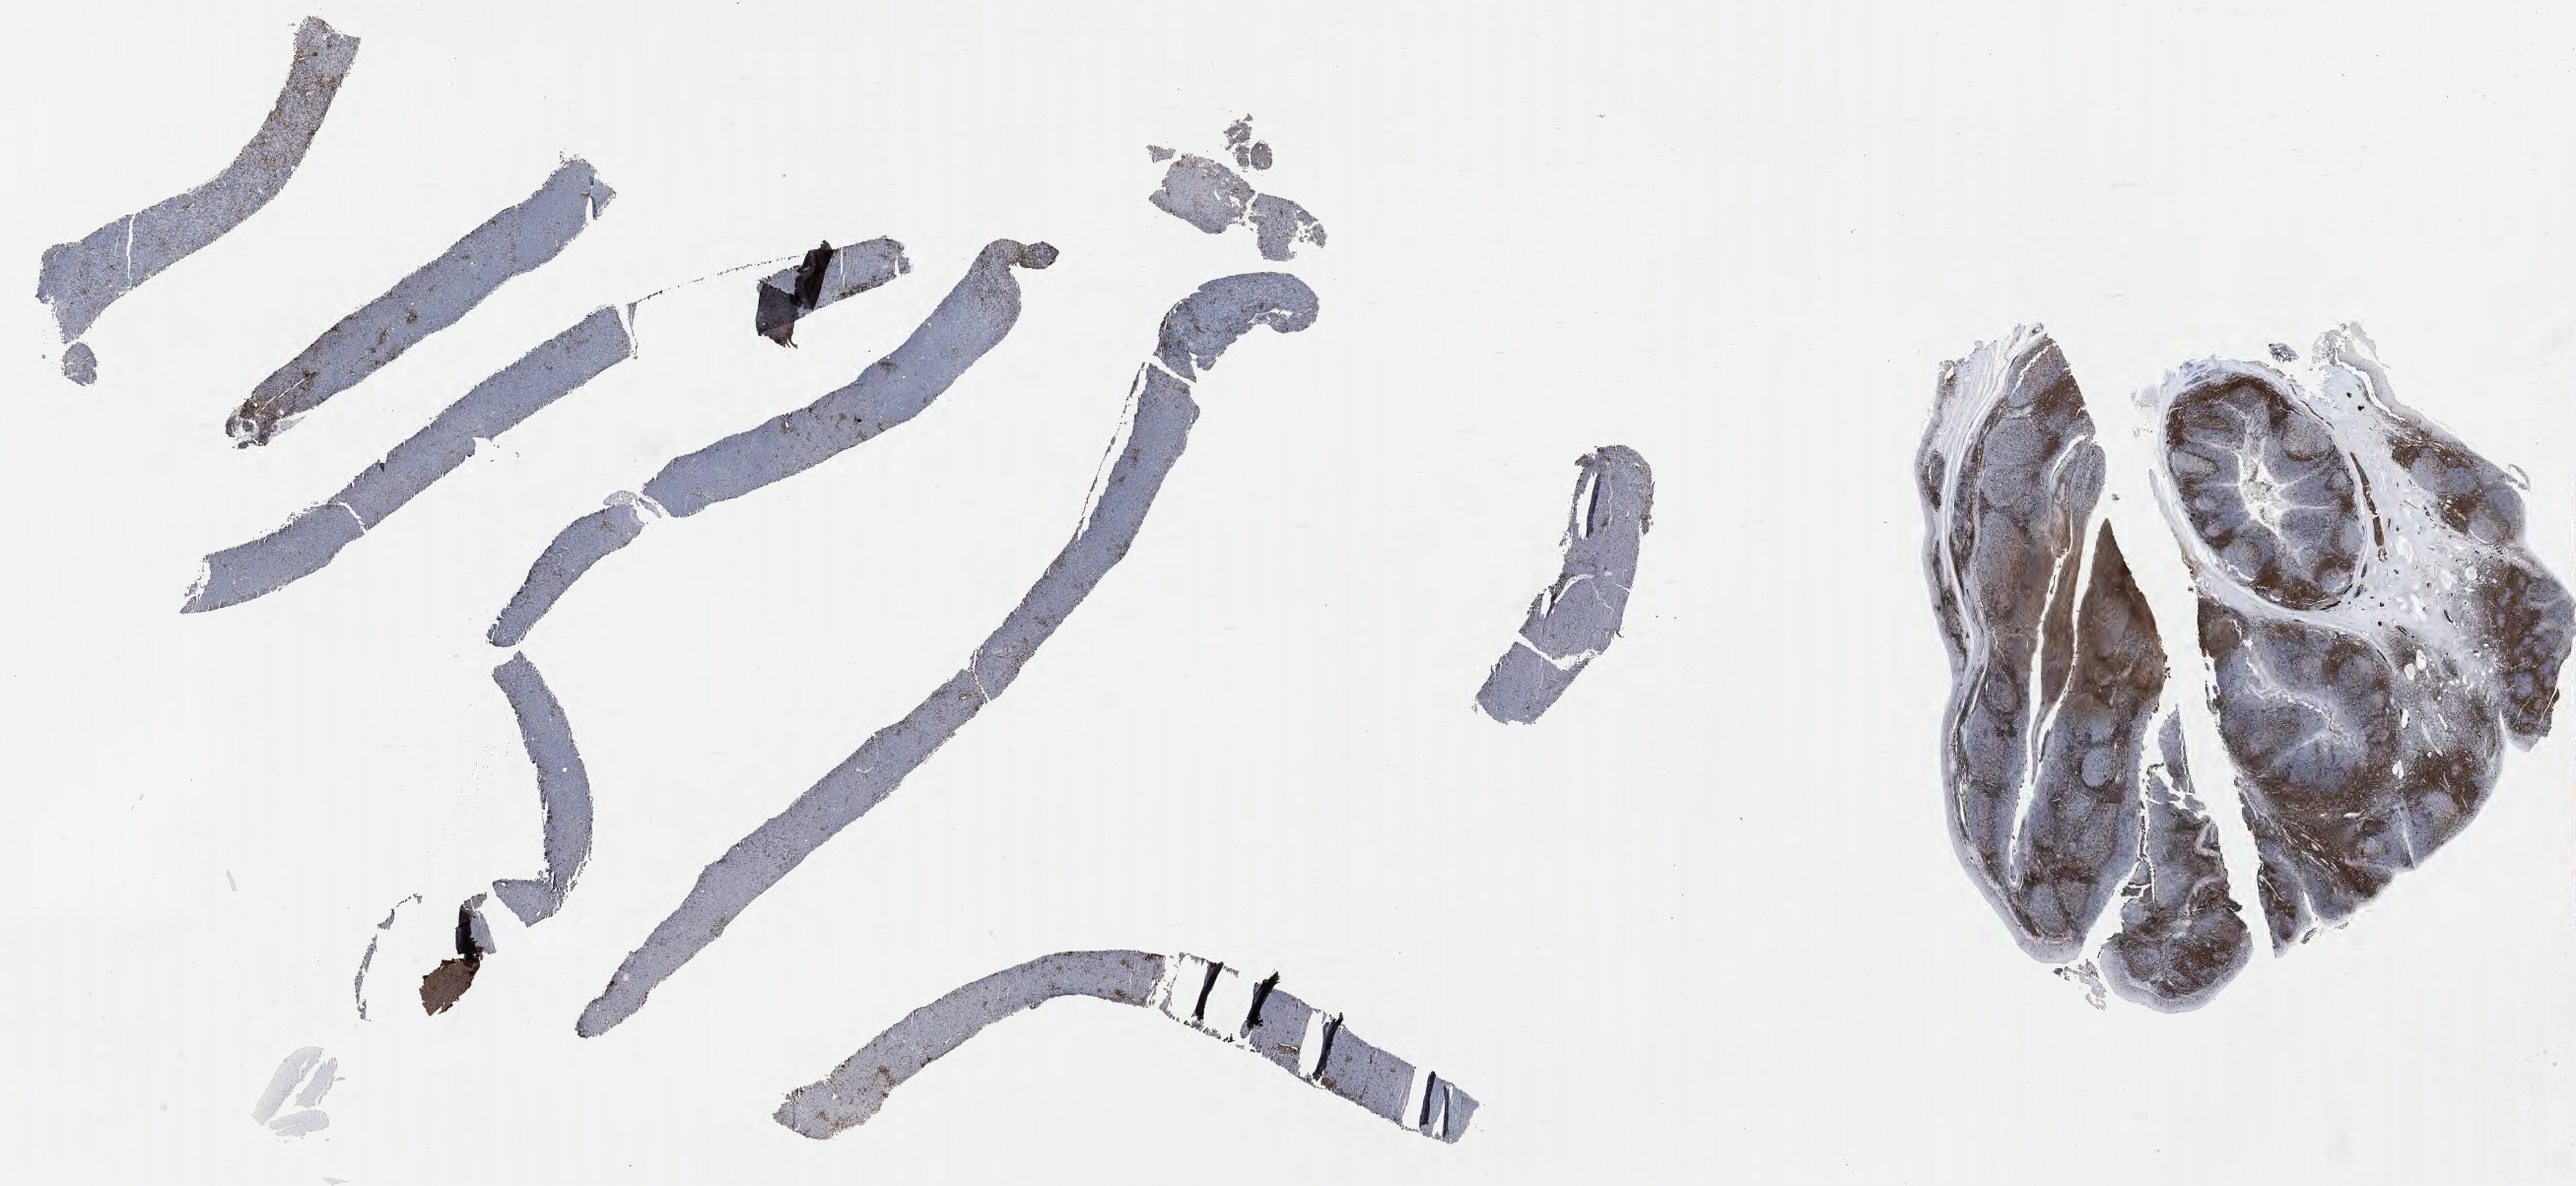
Whole-slide image, immunohistochemical stain for CD3 — low-resolution overview of the scanned area, about 42.3 x 19.5 mm. Specimen: tumor tissue. Patient: male, 29 years old.
Diagnosis: Burkitt lymphoma, NOS.